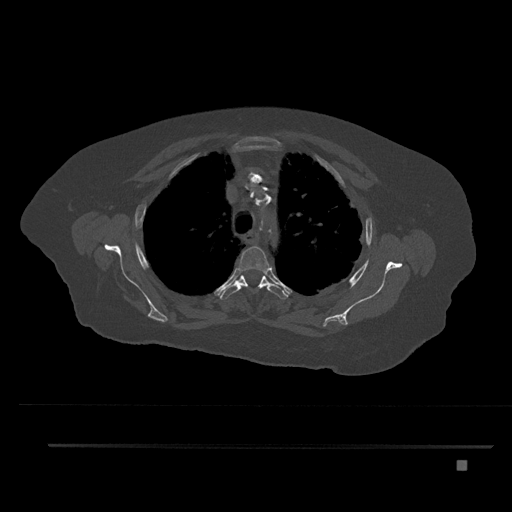
CT including the spine, one axial slice; position 618 of 797 along the scan axis; reconstruction kernel Br40s/3; 120 kVp; bone window (W 1800 / L 400 HU); 0.5 mm slice thickness; 512 × 512 image matrix, field of view 437 × 437 mm. Female patient, age 76 years. From the clinical record (not read from this slice): primary cancer: lung; vertebrae with lytic lesions (as recorded): T11, L3.
Structures marked on this image (semi-automatically segmented with operator editing):
- T3 vertebra: bounding box (x1, y1, x2, y2) in pixels: (232, 246, 272, 285)
- T4 vertebra: (219, 273, 289, 300)